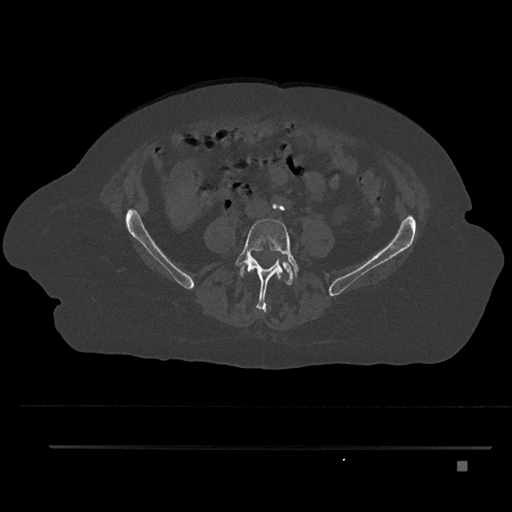
CT including the spine, one axial slice; slice 78 of 797 in the series (ordered by position); 120 kVp; bone window (W 1800 / L 400 HU); 0.5 mm slice thickness; 512 × 512 image matrix, field of view 437 × 437 mm. Patient: female, 76 years. From the clinical record (not read from this slice): primary cancer: lung; vertebrae with lytic lesions (as recorded): T11, L3.
Annotated regions visible in this slice (semi-automatic segmentation, software-assisted and operator-edited):
- L3 vertebra: box from (x=250, y=271) to (x=282, y=278) px
- L4 vertebra: (x=234, y=218)–(x=300, y=312)
- L5 vertebra: (x=240, y=262)–(x=297, y=285)